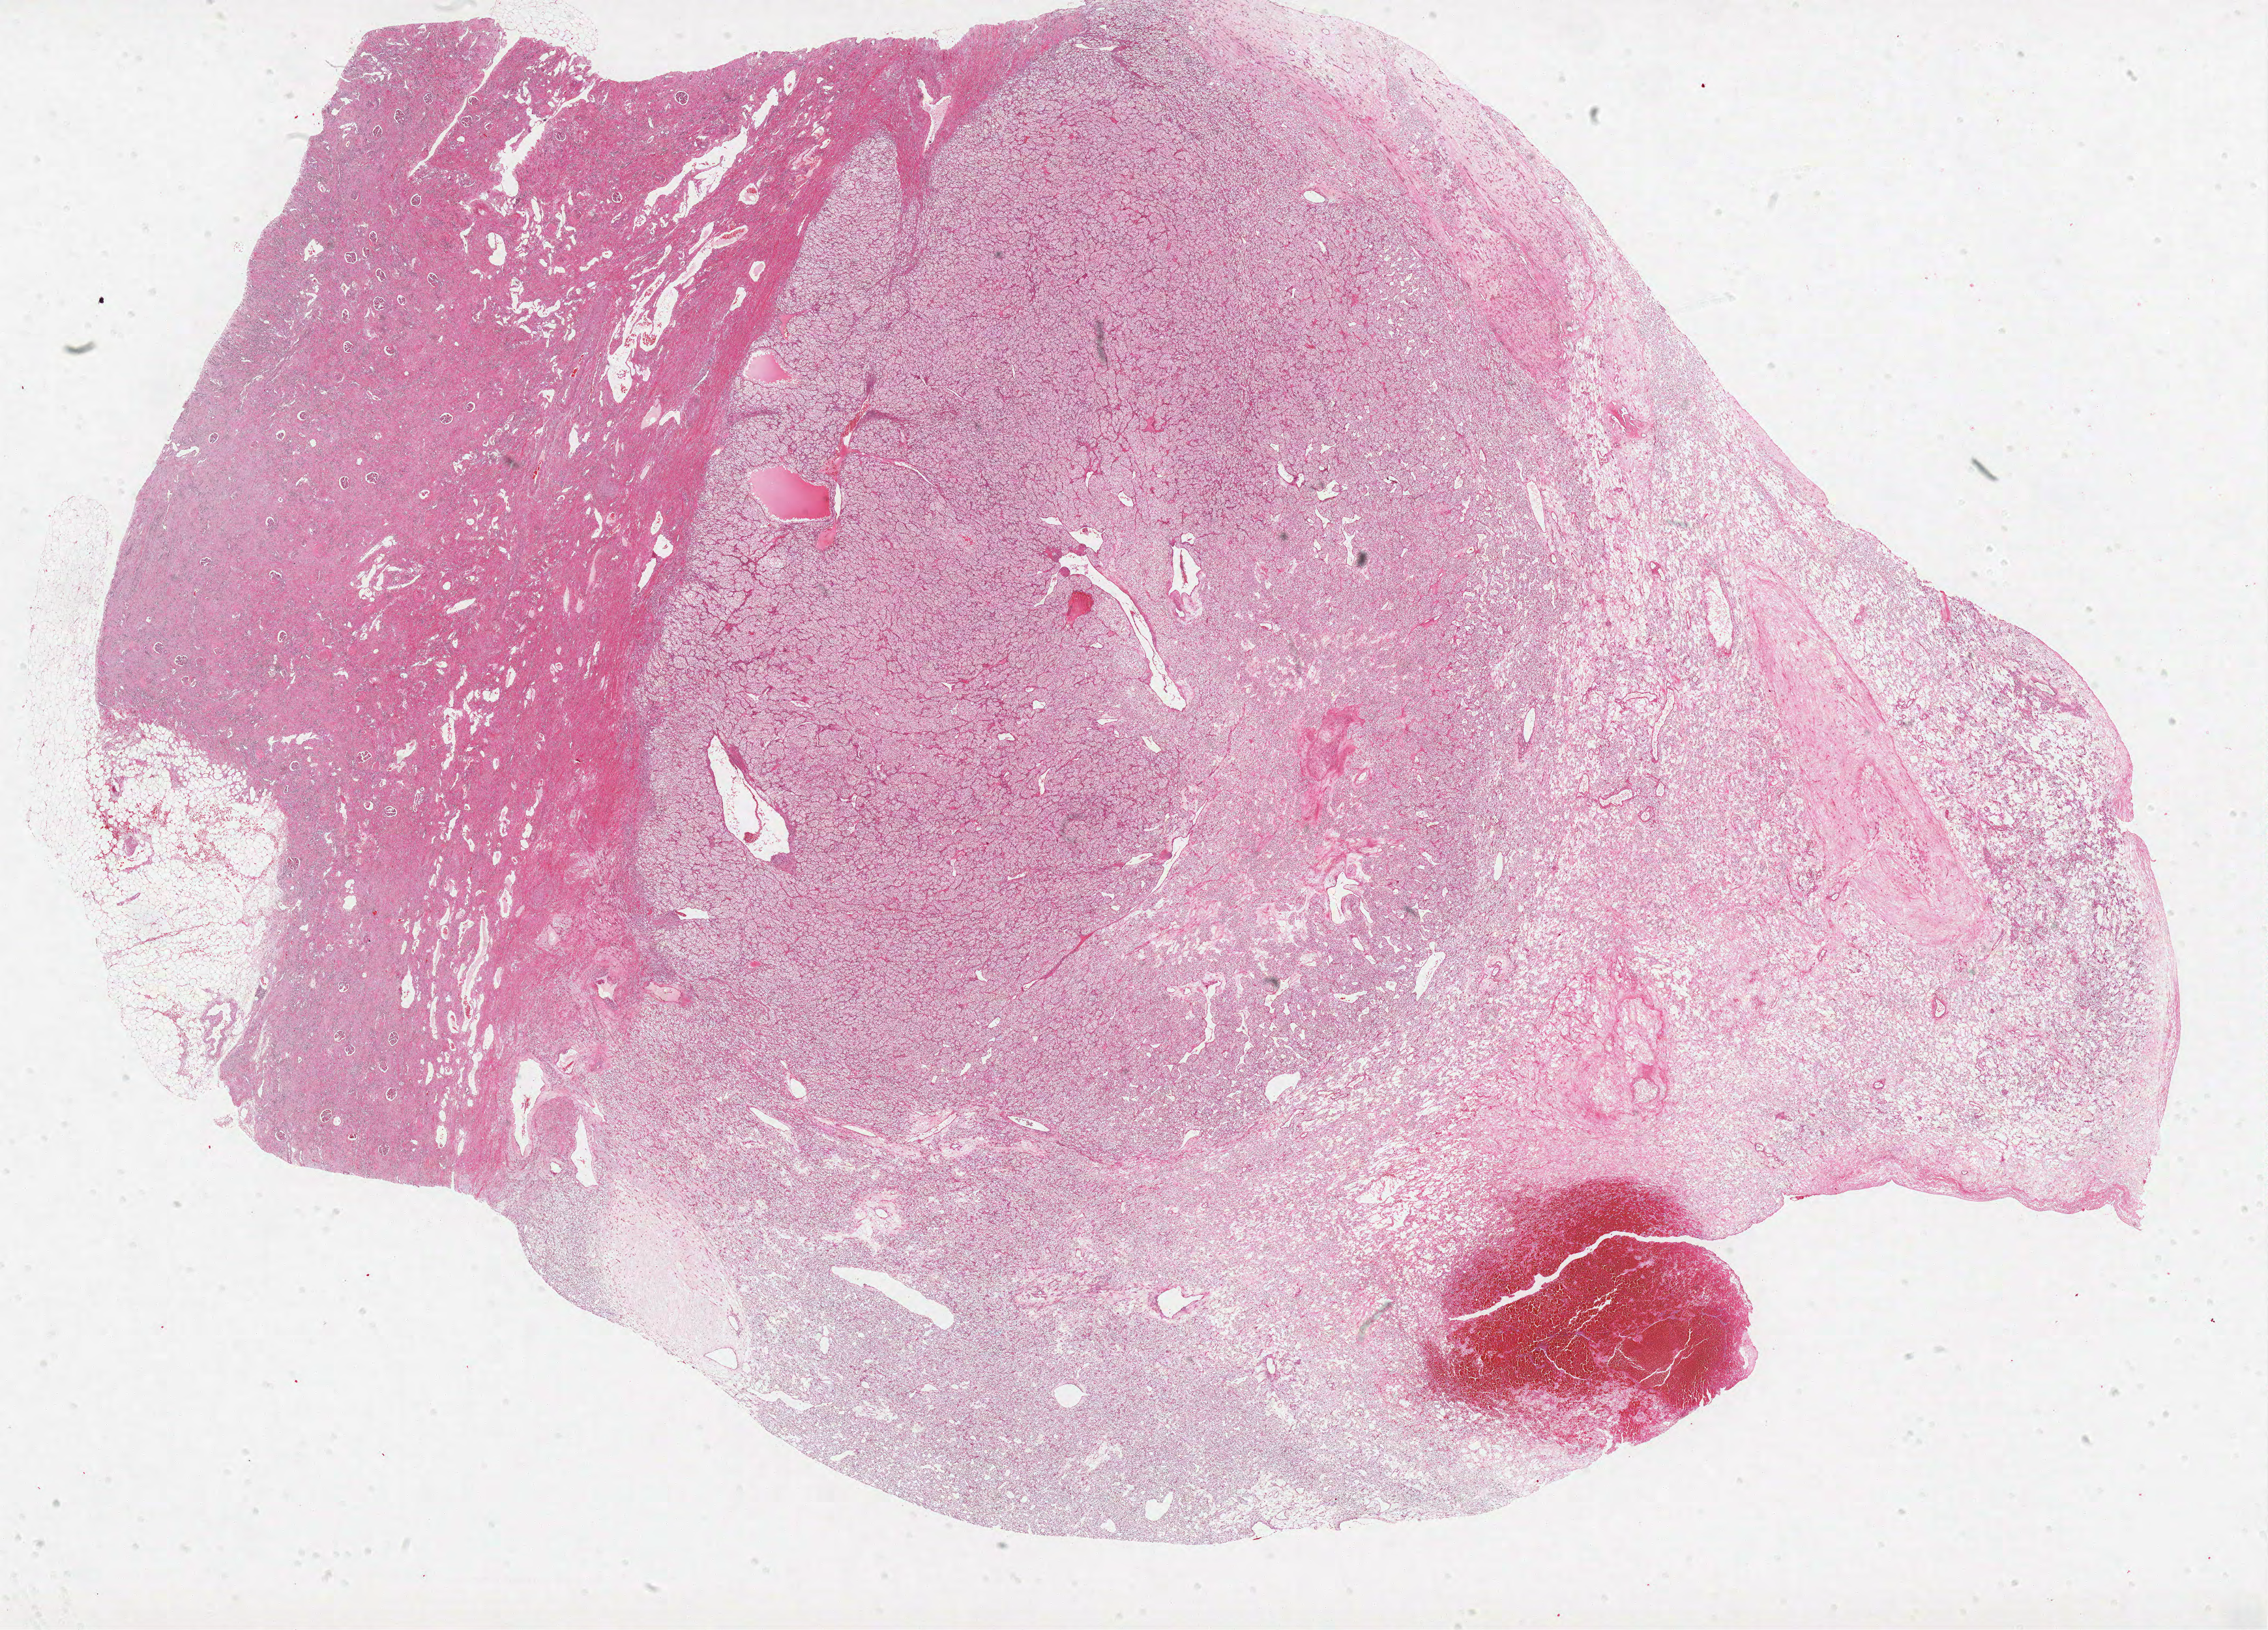
H&E-stained whole-slide image, shown as a low-resolution overview of the whole scanned area (about 27.8 x 20.0 mm, from a 40x scan), FFPE section, sample: primary tumour, kidney. Female, age 64 years at initial diagnosis. Histologic grade: G1 (well differentiated).
AJCC pathologic stage: I. Pathologic diagnosis: Clear cell adenocarcinoma, NOS.